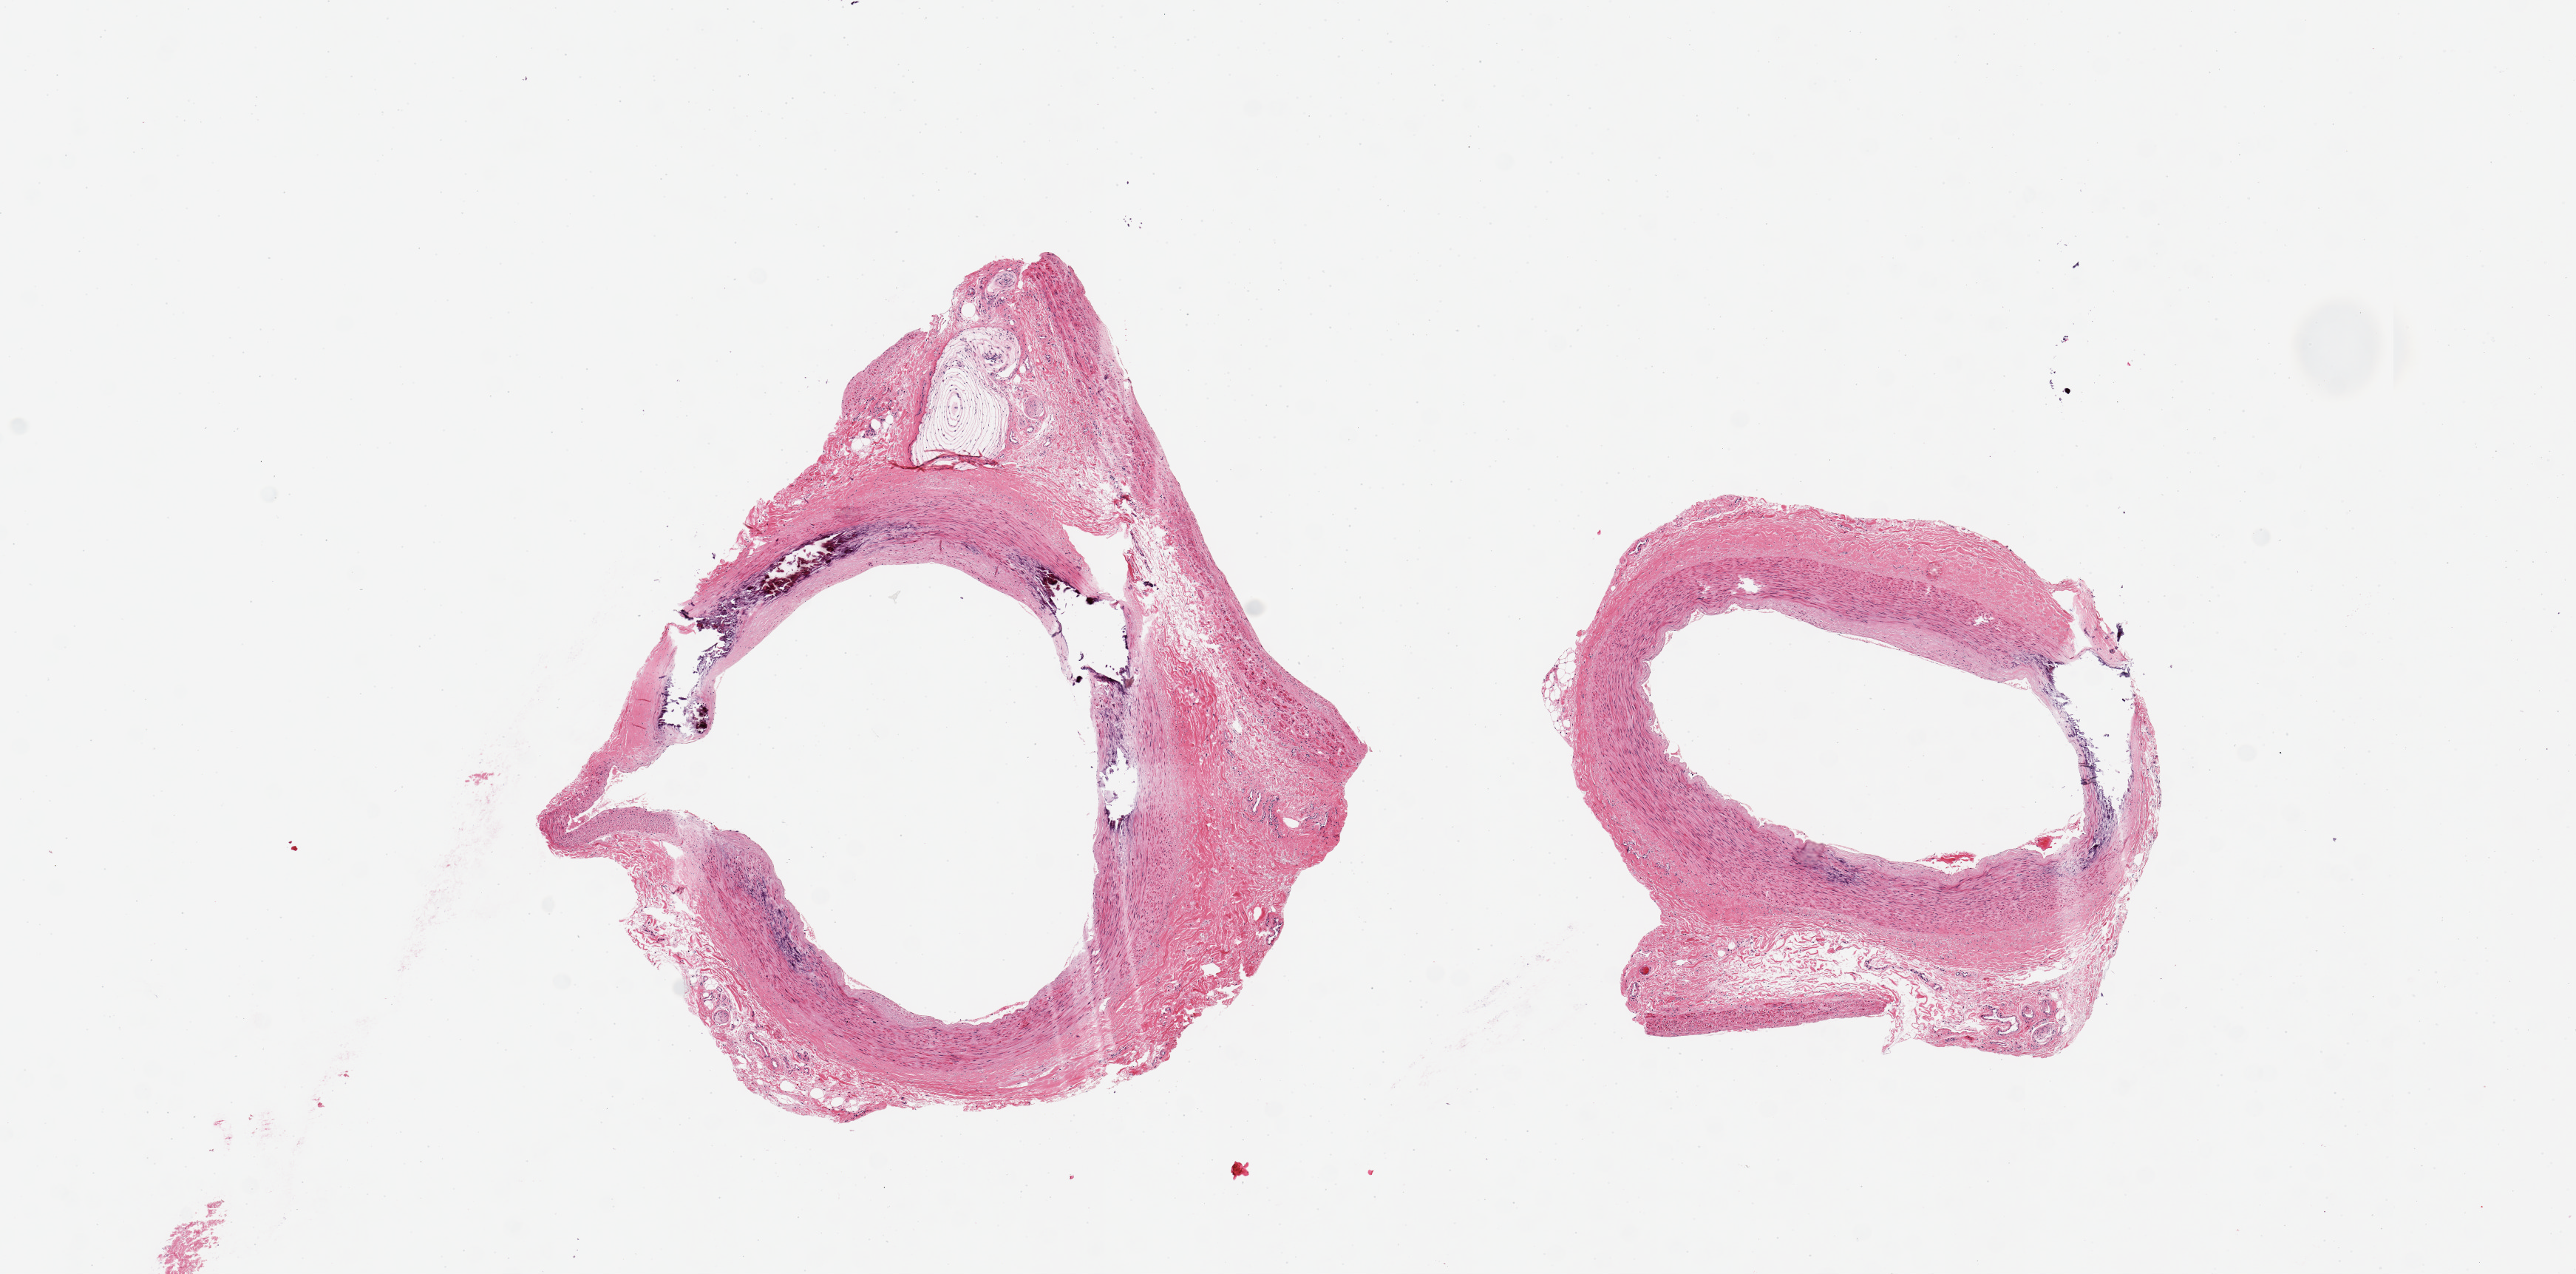
Whole-slide image, H&E stain, a low-resolution overview of the entire scanned area, about 13.8 x 6.8 mm (from a 20x scan). PAXgene-fixed, paraffin-embedded tissue. Section of tibial artery (target tissue). Tissue donor sample. Donor: female.
Review note (as recorded): 2 pieces, 4x4 & 3x3 mm arteries; one with medial calcification.